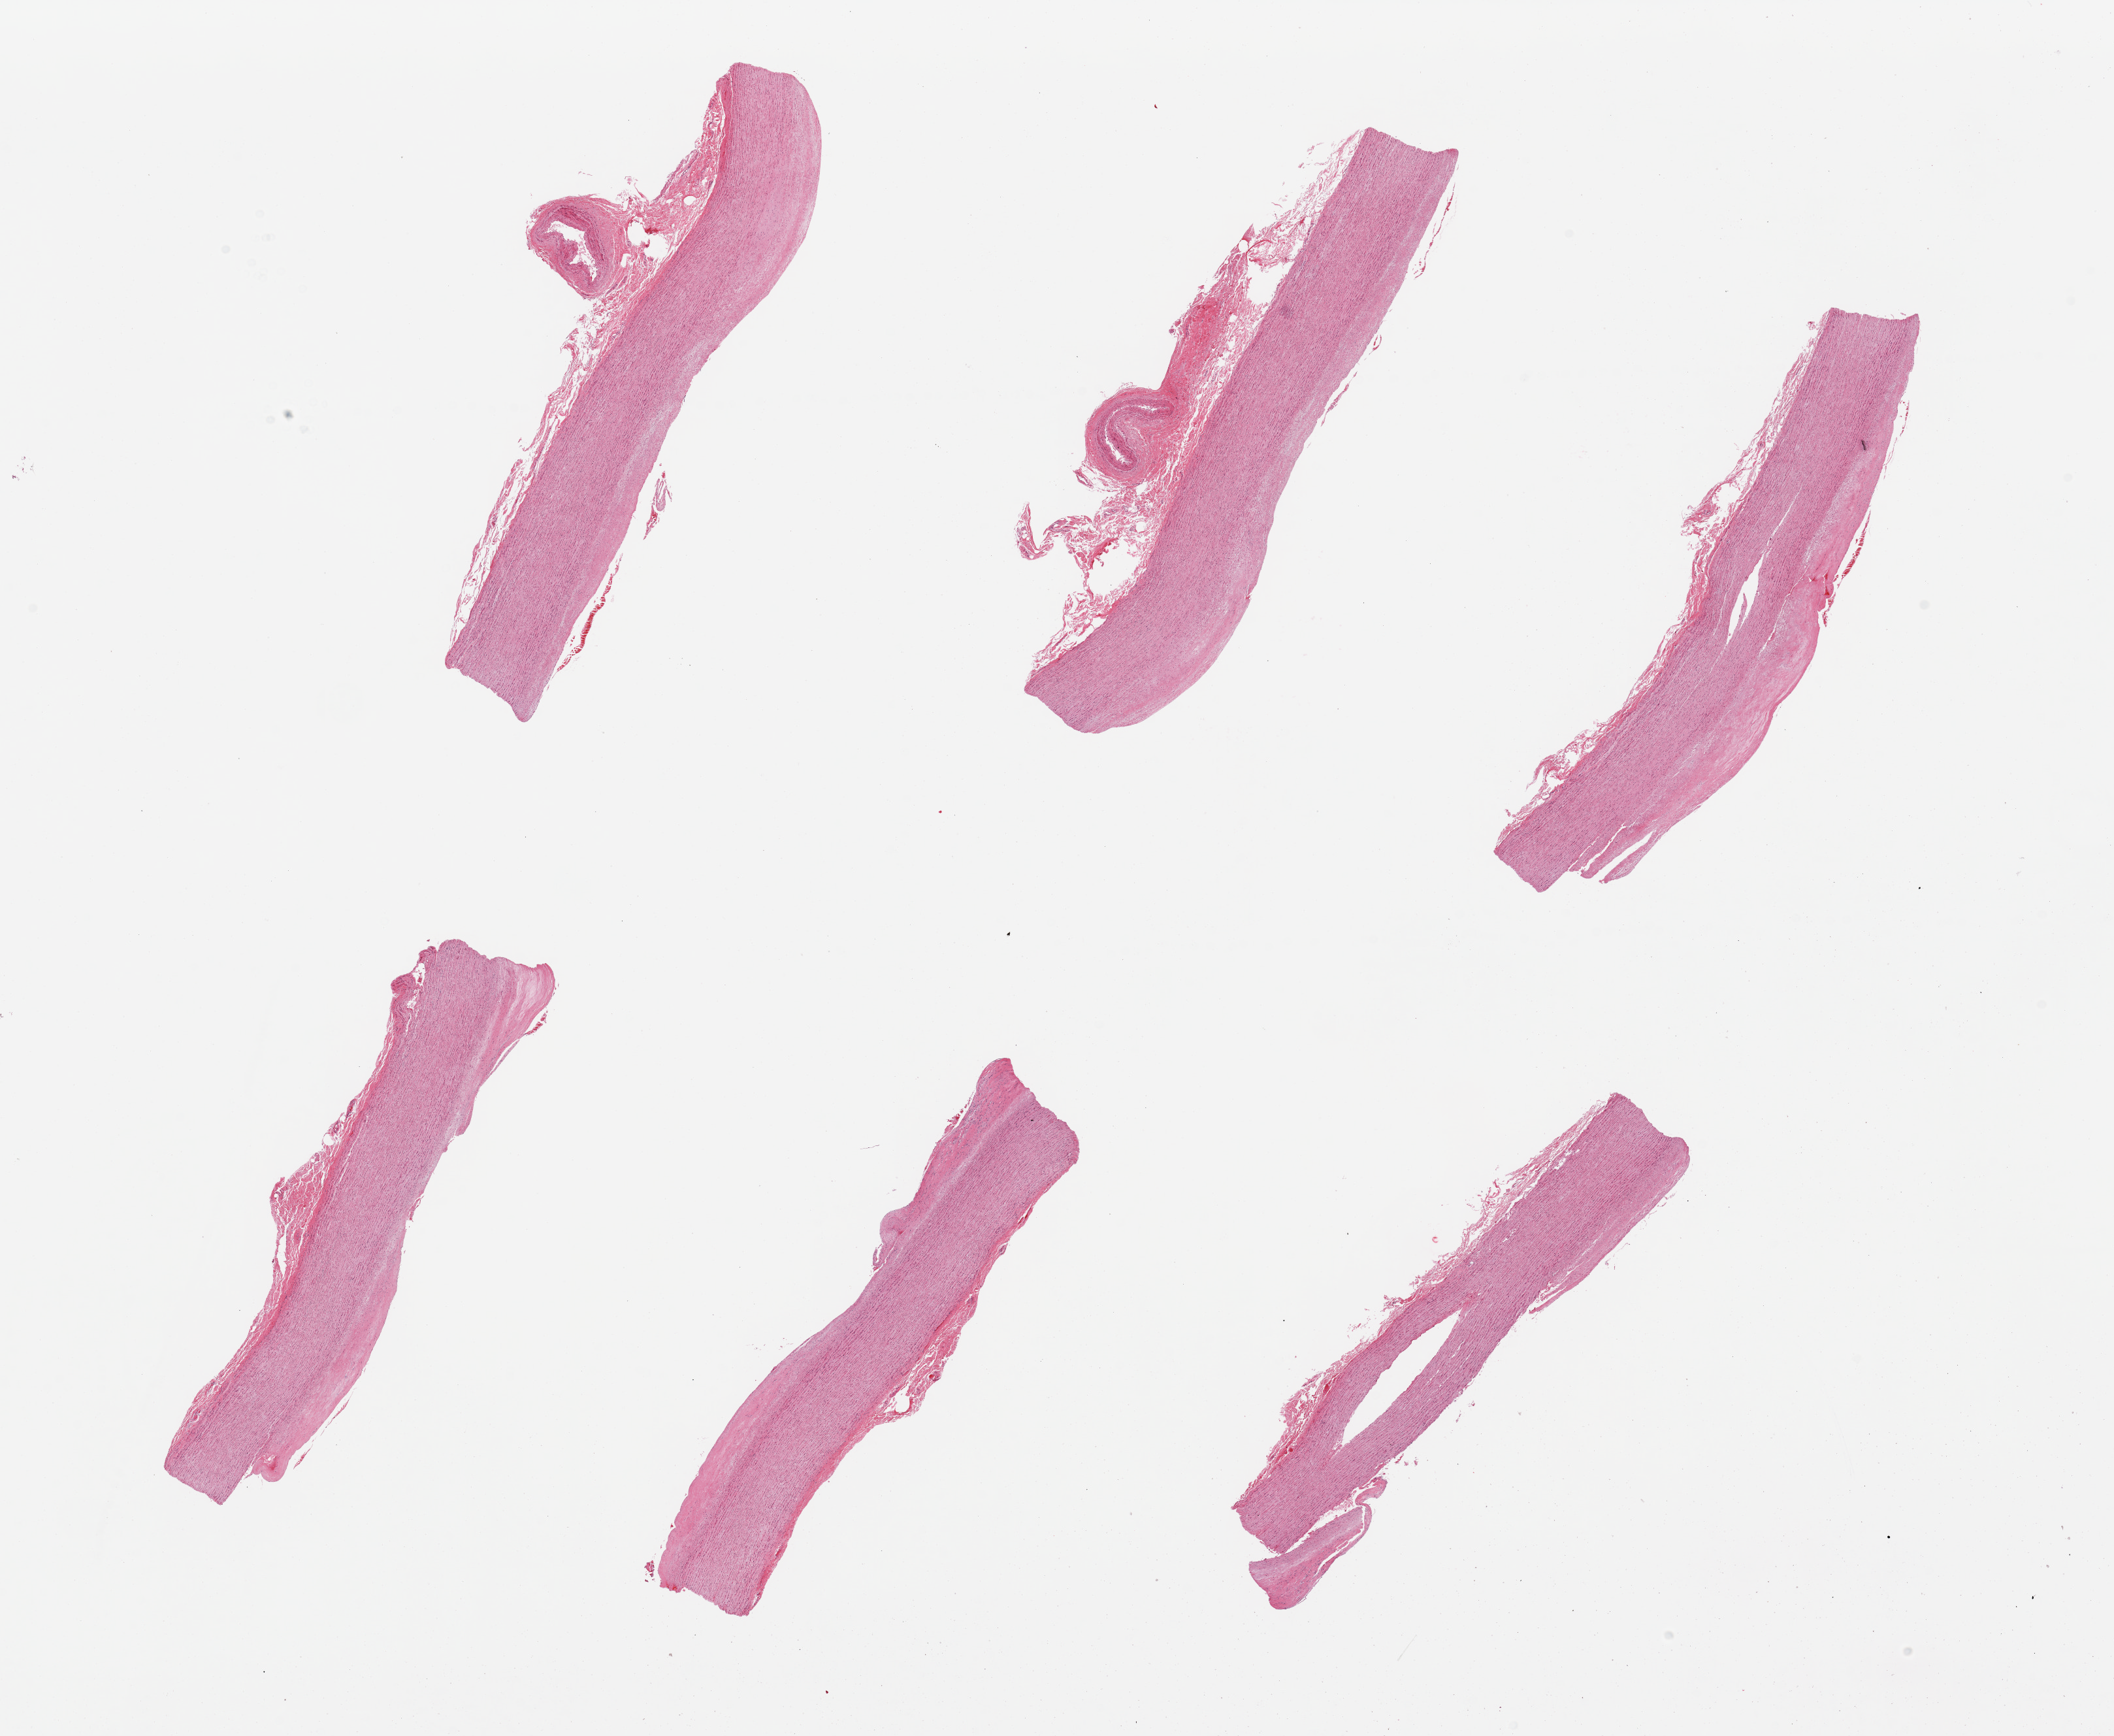
H&E whole-slide image — shown as a low-resolution overview of the whole scanned area (about 25.6 x 21.0 mm); PAXgene-fixed paraffin-embedded (PFPE) section; section of aorta (target tissue); donor tissue sample.
Reviewer comment on this tissue sample: 6 pieces, atherosis up to ~1mm; adherent serosa, vasa vasorum.